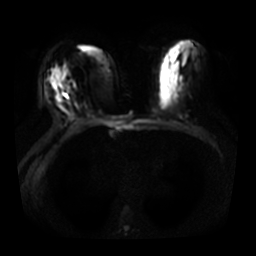
Breast MRI, one axial slice; slice 16 of 31 in the series (ordered by position); diffusion-weighted series; image 2 of 4 stored at this slice position (different b-values; order by instance number); 3 T; 256 × 256 image matrix, field of view 350 × 350 mm. Female patient.
Annotated regions visible in this slice (manually delineated by an expert):
- tumour on diffusion-weighted imaging: box from (x=52, y=69) to (x=62, y=89) px